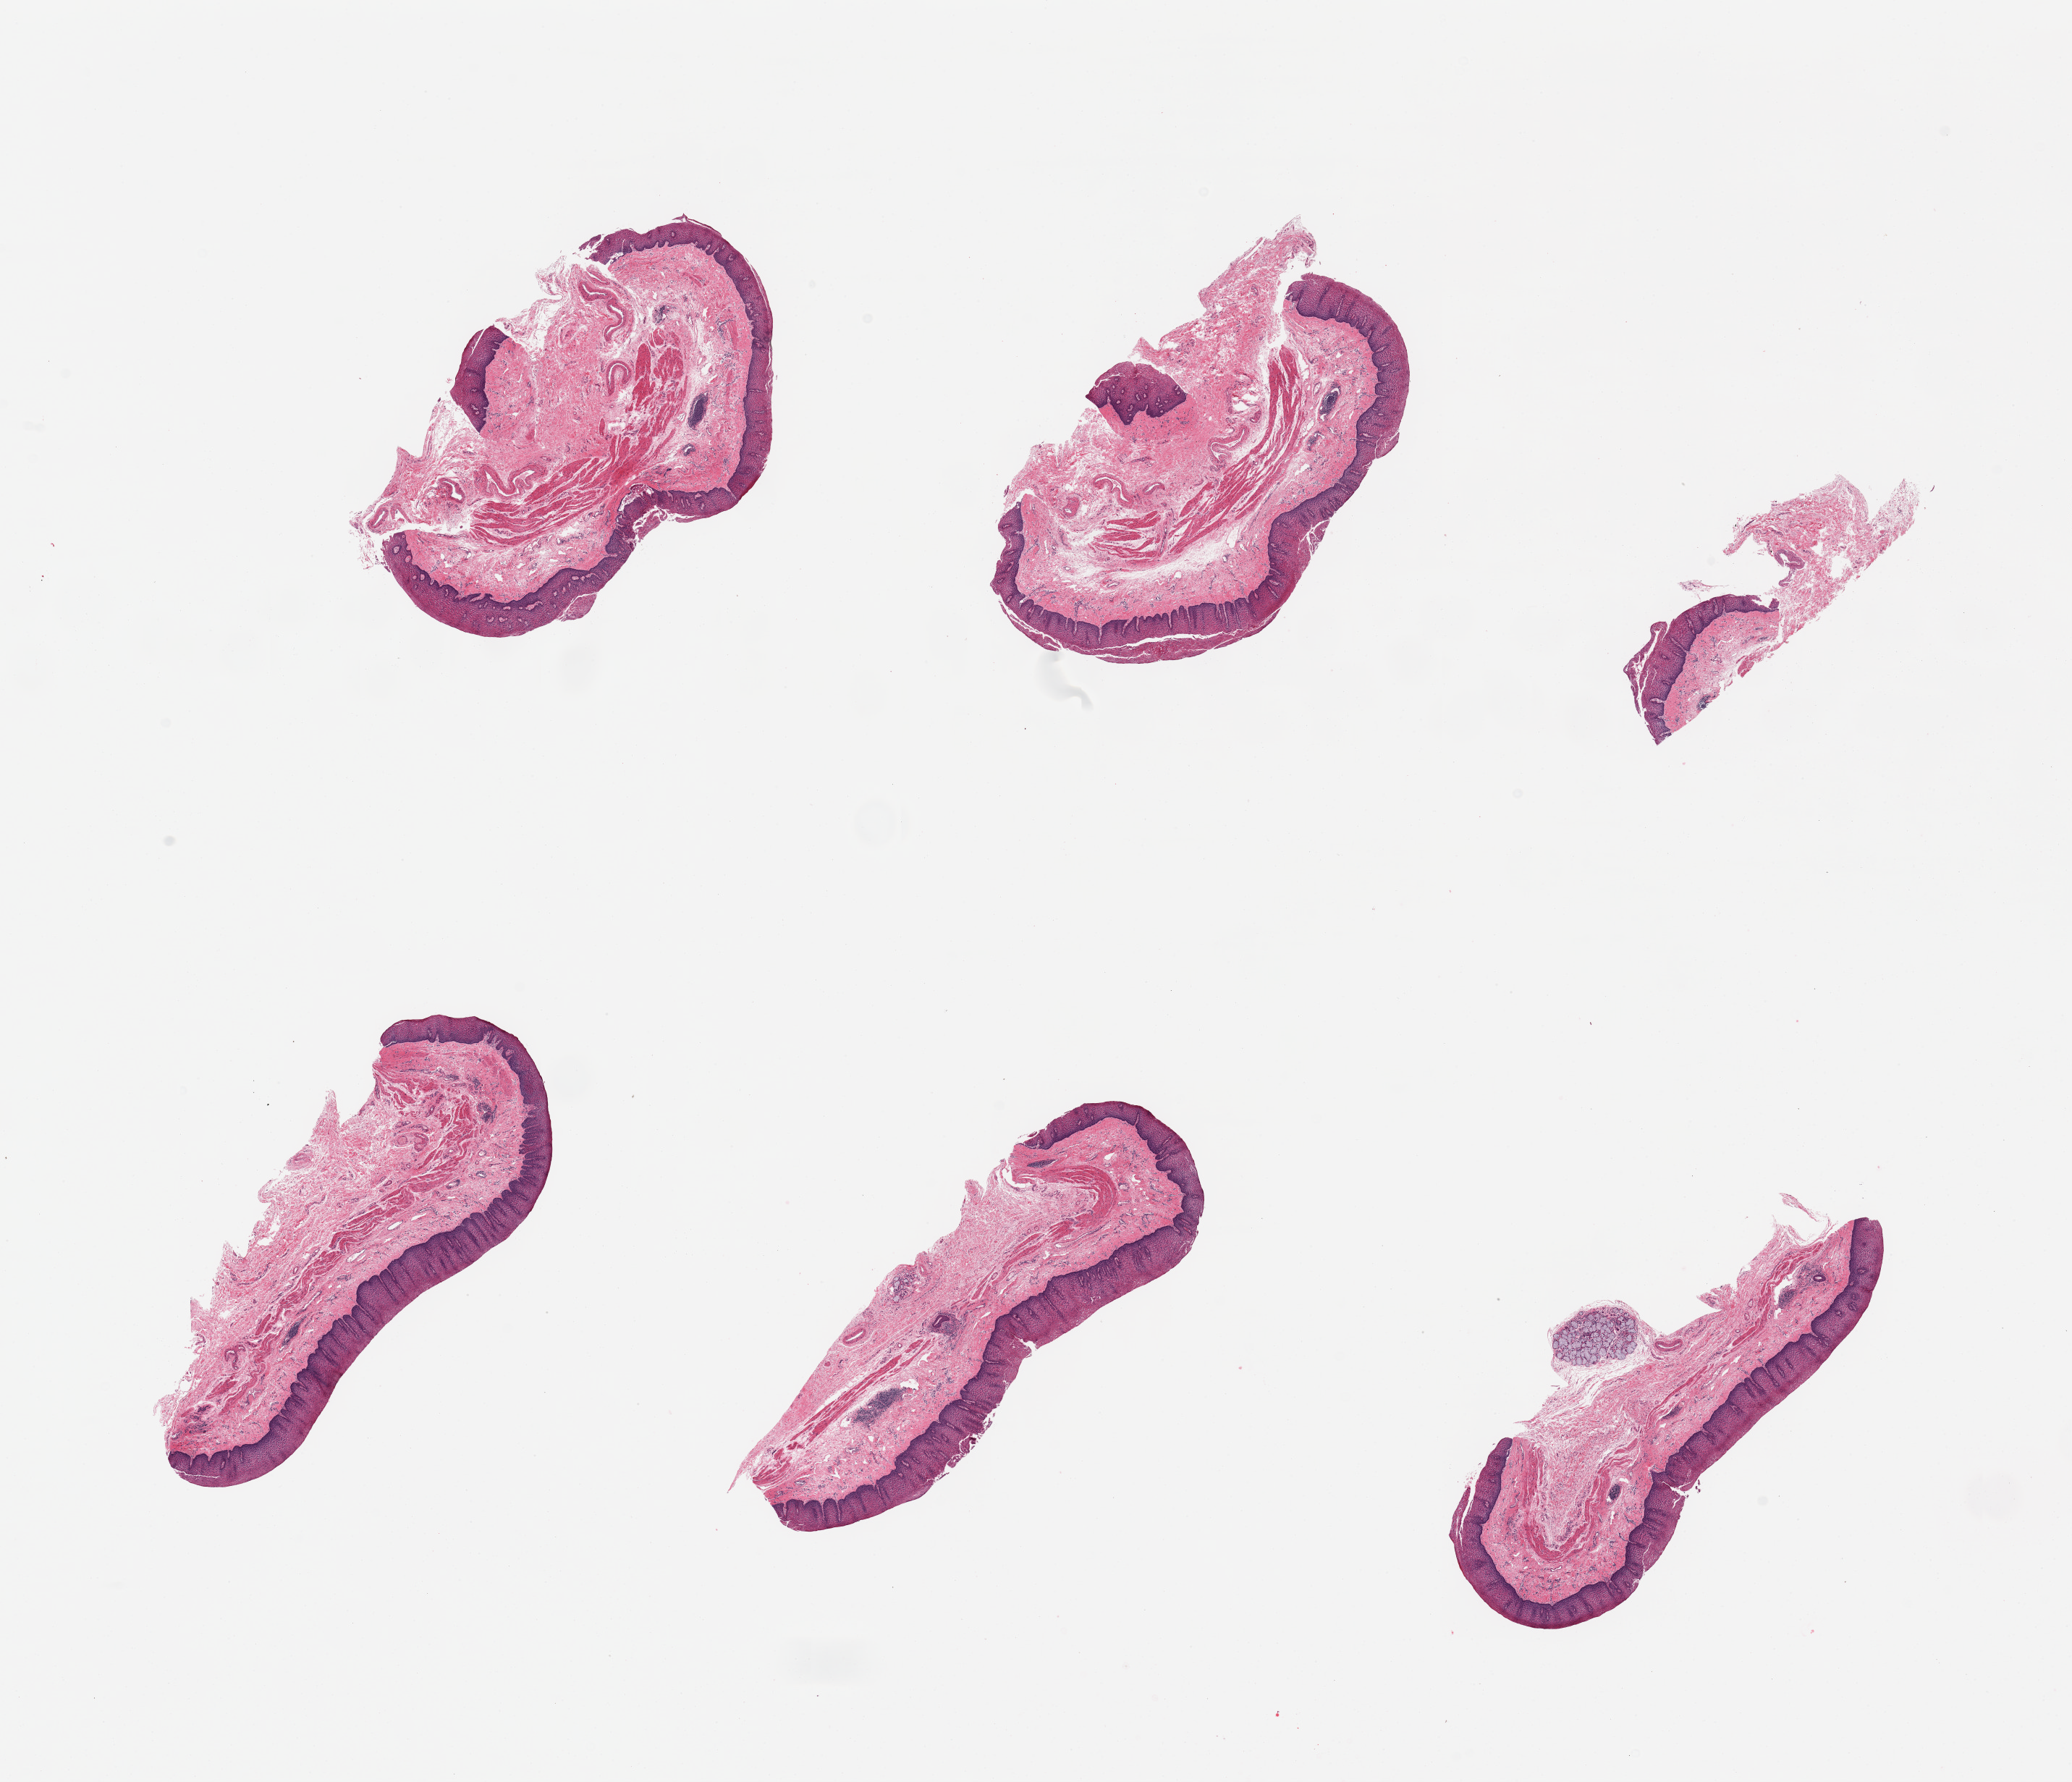
Whole-slide image, hematoxylin and eosin (H&E) stain — whole scanned area (about 22.6 x 19.5 mm) shown as a low-resolution overview; PAXgene-fixed, paraffin-embedded tissue; section of esophageal mucous membrane (target tissue); tissue donor sample.
Review note (as recorded): 6 pieces, squamous mucosa up to ~0.5mm, ~30% thickness; few submucosal mucus glands noted.